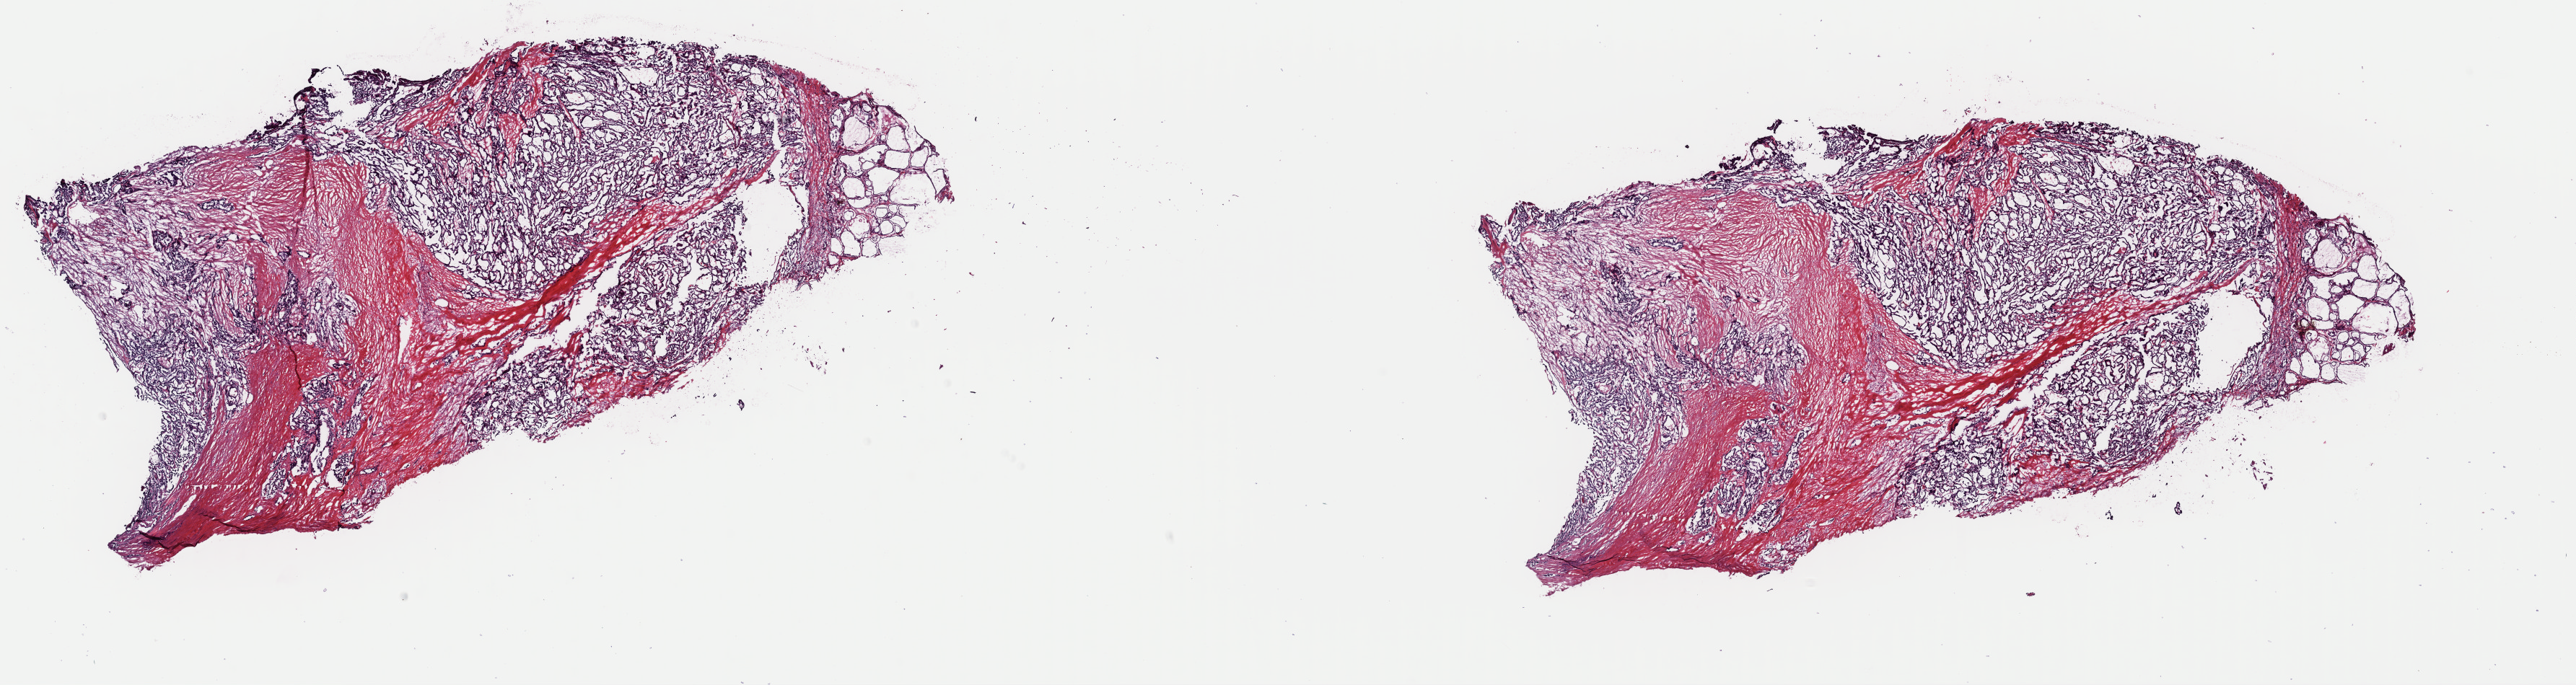
H&E whole-slide image, shown as a low-resolution overview of the whole scanned area (about 28.2 x 7.5 mm); frozen section; thyroid, primary tumour sample. Female, age 57 years at initial diagnosis. Slide review estimates, as recorded: tumour cells 65%, tumour nuclei 75%, normal cells 5%, stromal cells 30%, necrosis 0%. Infiltration values recorded for this section: lymphocyte infiltration 2%, monocyte infiltration 0%, neutrophil infiltration 0%.
Pathologic diagnosis: Papillary adenocarcinoma, NOS (thyroid gland). AJCC pathologic stage: I (7th edition).